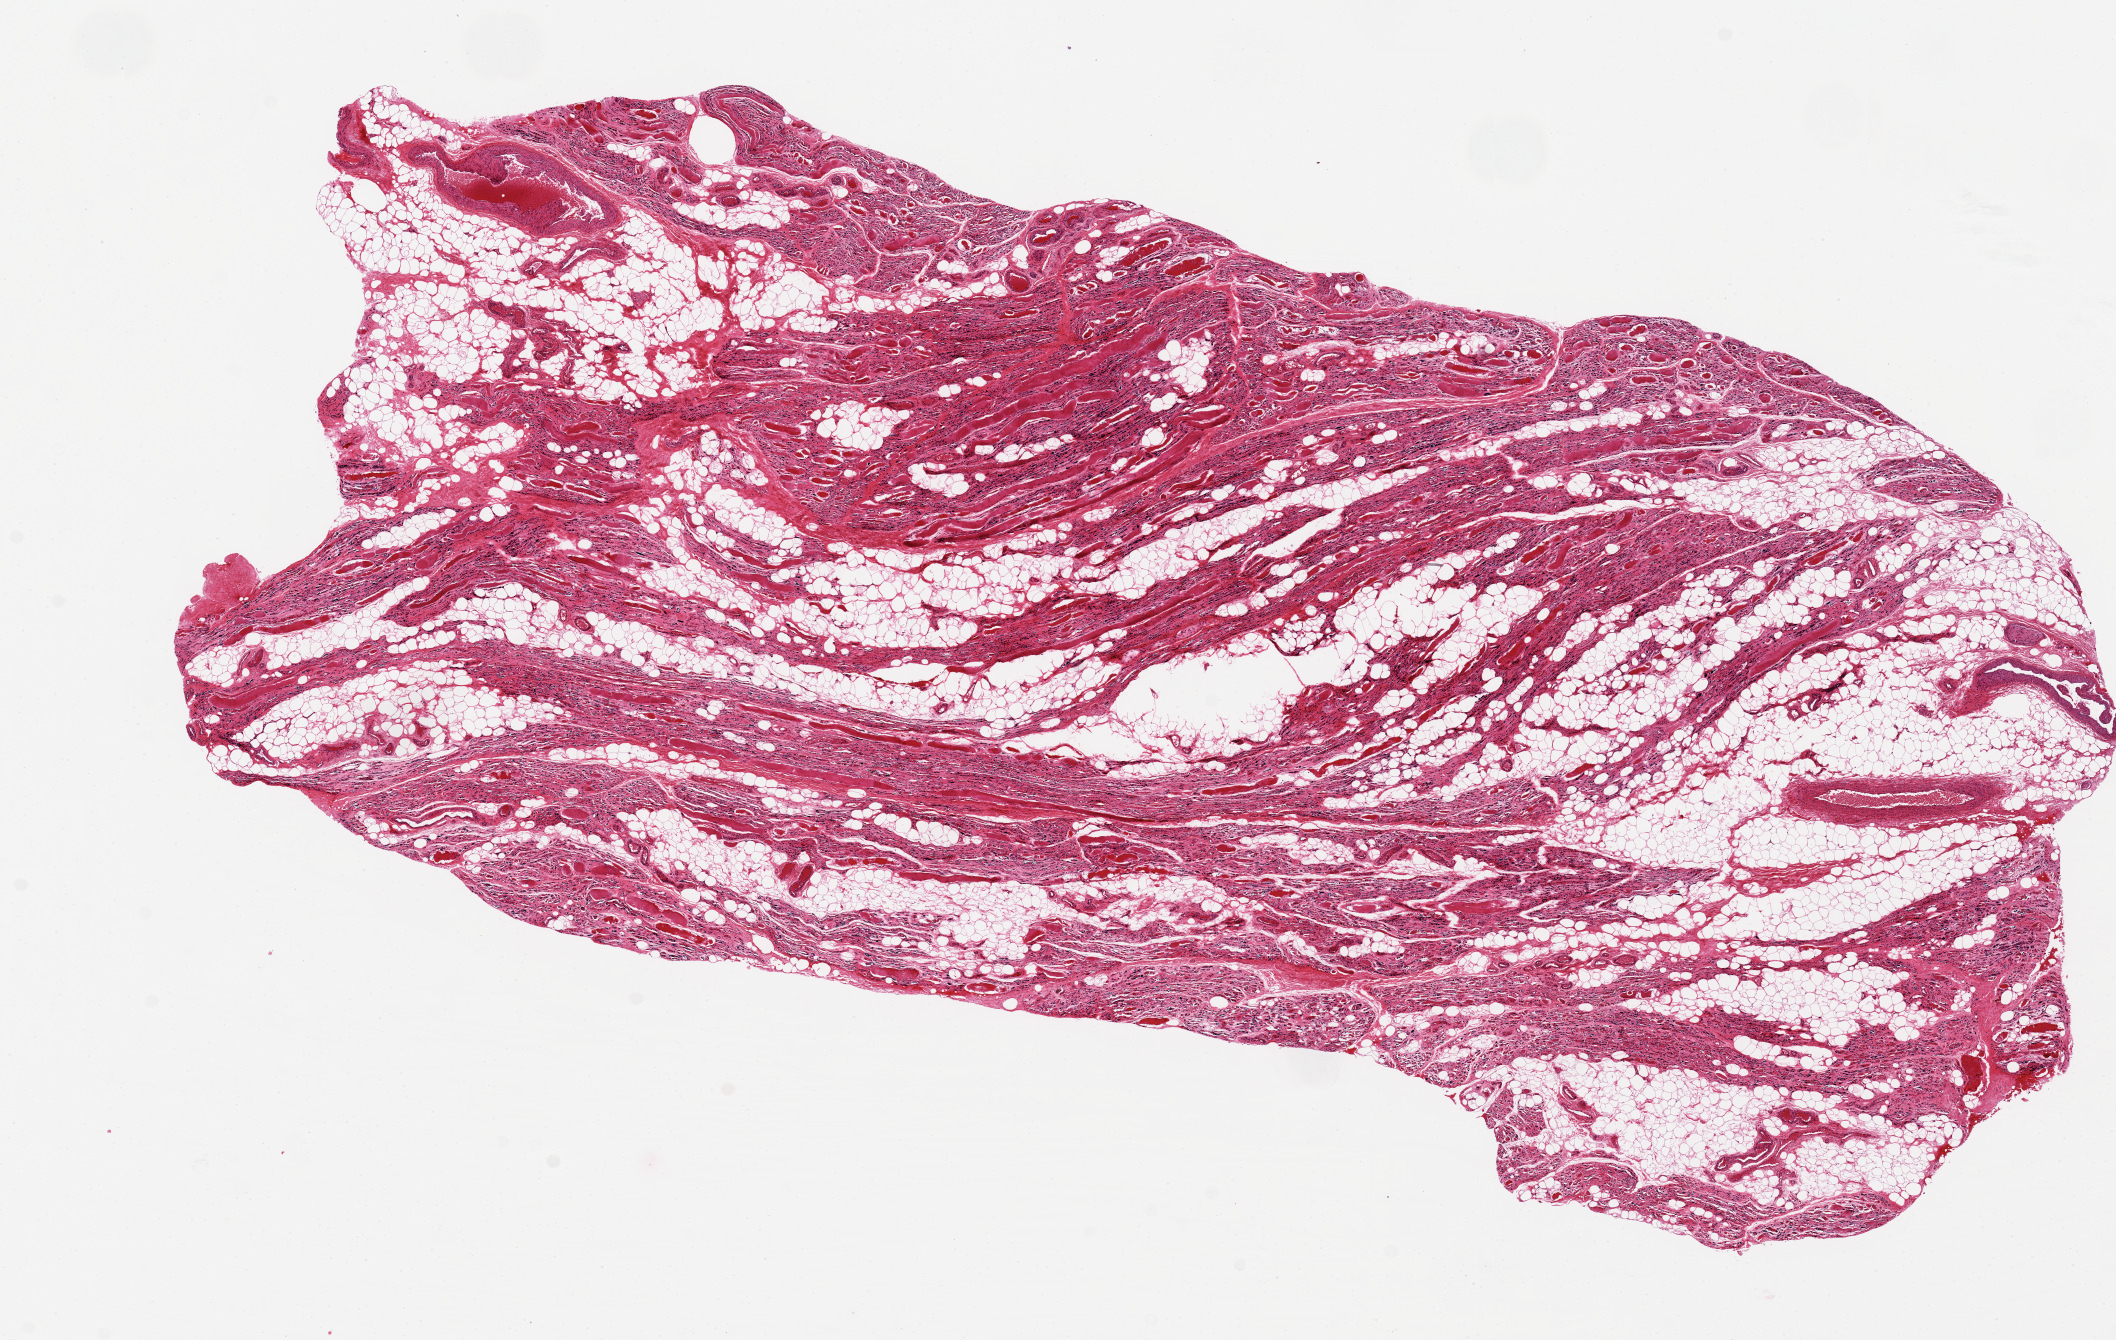
H&E whole-slide image, shown as a low-resolution overview of the whole scanned area (about 16.7 x 10.6 mm). PAXgene-fixed, paraffin-embedded tissue. Sampled site (target tissue): skeletal muscle. Donor tissue sample. Donor: female.
• review note (as recorded): Severe atrophy, fibrosis, and fatty infiltration (>50%) with scattered hypertrophic fibers. 14.4x6.8mm